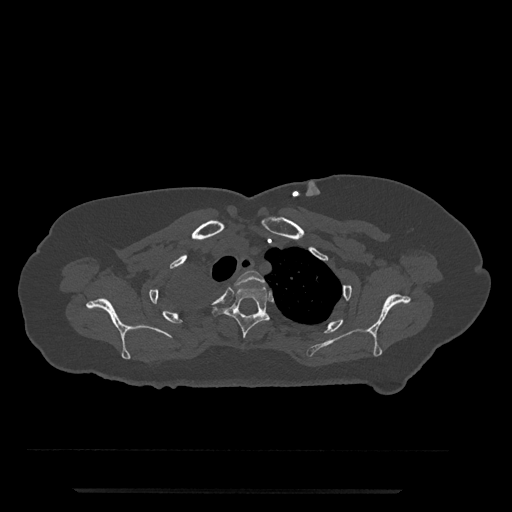
CT including the spine, one axial slice. Slice 636 of 797 in the series (ordered by position). Reconstruction kernel Br40s/3. 120 kVp. Bone window (W 1800 / L 400 HU). 0.5 mm slice thickness. 512 × 512 image matrix, field of view 440 × 440 mm. Female patient, age 51 years. Case-level facts recorded for this patient, not image findings: primary cancer: neuro; vertebrae with lytic lesions (as recorded): T8.
Outlined on this slice (semi-automatic segmentation, software-assisted and operator-edited):
- T2 vertebra: bounding box <230,270,265,301> (left, top, right, bottom; pixels)
- T3 vertebra: <213,286,269,338>